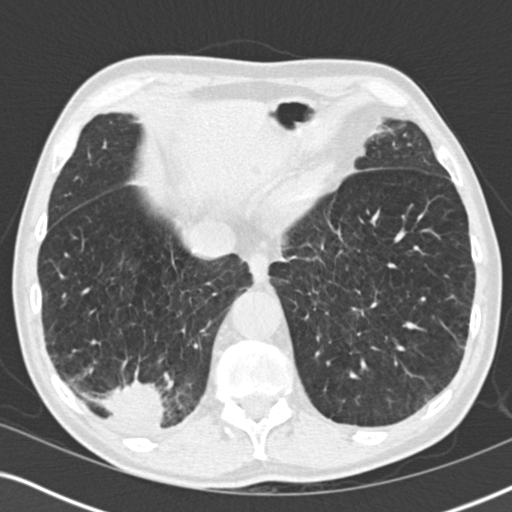
Axial slice from a low-dose chest CT screening exam. First (baseline) screen. Lung window (W 1500 / L -600 HU). Standard (soft-tissue) reconstruction kernel (B30f). Slice 142 of 196 in the series. 512 × 512 image matrix, field of view 330 × 330 mm. Male participant, aged 64 years at enrolment. Former smoker at enrolment.
- Expert reader's lesion annotation, bounding box [x1, y1, x2, y2] px = [79, 366, 179, 451].
- The screening reader recorded 3 non-calcified nodules or masses ≥4 mm on this exam (lingula, lingula, right lower lobe); which of them this box marks is not recorded.
- Participant outcome: lung cancer diagnosed 27 days after this screen — squamous cell carcinoma, NOS, right lower lobe, moderately differentiated (G2), stage IV (AJCC 6th edition), 40 mm at pathology.